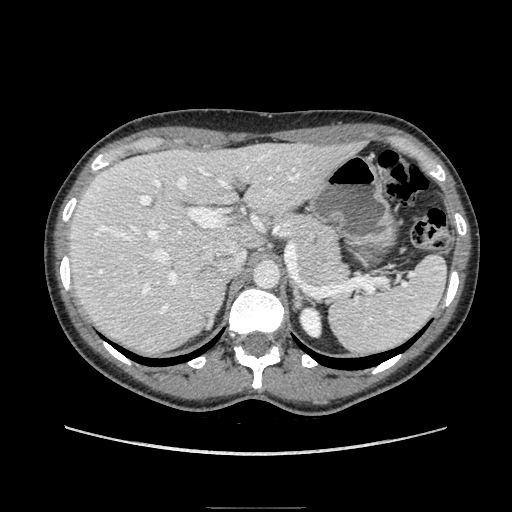
Contrast-enhanced abdominal CT, one axial slice. Position 123 of 193 along the scan axis. Soft-tissue window (W 400 / L 40 HU). 1.25 mm slice thickness. 512 × 512 image matrix, field of view 380 × 380 mm. Female patient. Case-level facts recorded for this patient, not image findings: diagnosis: adrenocortical carcinoma; tumour side: right adrenal; tumour size at pathology: 3 cm; Ki-67 index: 4 %; stage (as recorded): 1.
Structures marked on this image (semi-automatic segmentation, software-assisted and operator-edited):
- mass: bounding box [x1, y1, x2, y2] px = [192, 267, 225, 326]